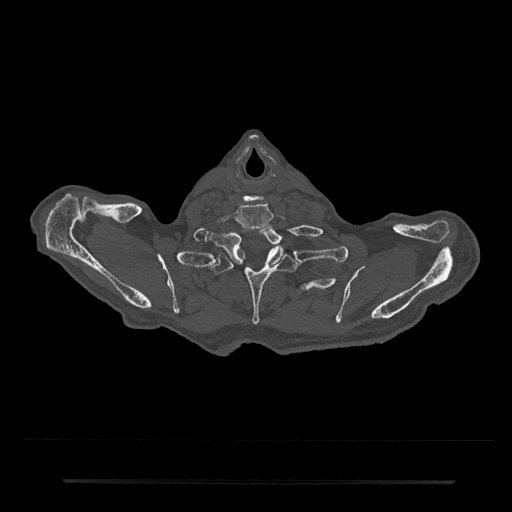
CT including the spine, one axial slice. 120 kVp. Bone window (W 1800 / L 400 HU). 0.5 mm slice thickness. 512 × 512 image matrix, field of view 427 × 427 mm. Patient: male, 74 years. From the clinical record (not read from this slice): primary cancer: prostate.
Structures marked on this image (semi-automatic segmentation, software-assisted and operator-edited):
- T1 vertebra: bounding box (x1, y1, x2, y2) in pixels: (212, 224, 284, 266)
- T2 vertebra: (210, 248, 303, 325)
- T3 vertebra: (294, 290, 296, 293)